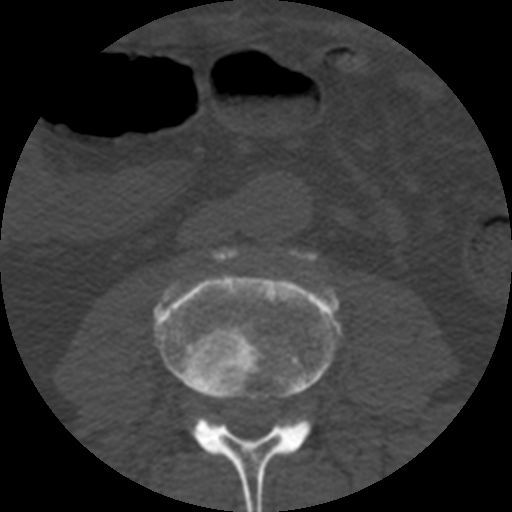
CT including the spine, one axial slice; slice 115 of 508 in the series (ordered by position); reconstruction kernel STANDARD; bone window (W 1800 / L 400 HU); 1.25 mm slice thickness; 512 × 512 image matrix. Patient age 57 years. From the clinical record (not read from this slice): primary cancer: prostate.
Structures marked on this image (semi-automatic segmentation, software-assisted and operator-edited):
- L3 vertebra: bounding box (x1, y1, x2, y2) in pixels: (155, 273, 340, 512)
- L4 vertebra: (216, 248, 315, 261)